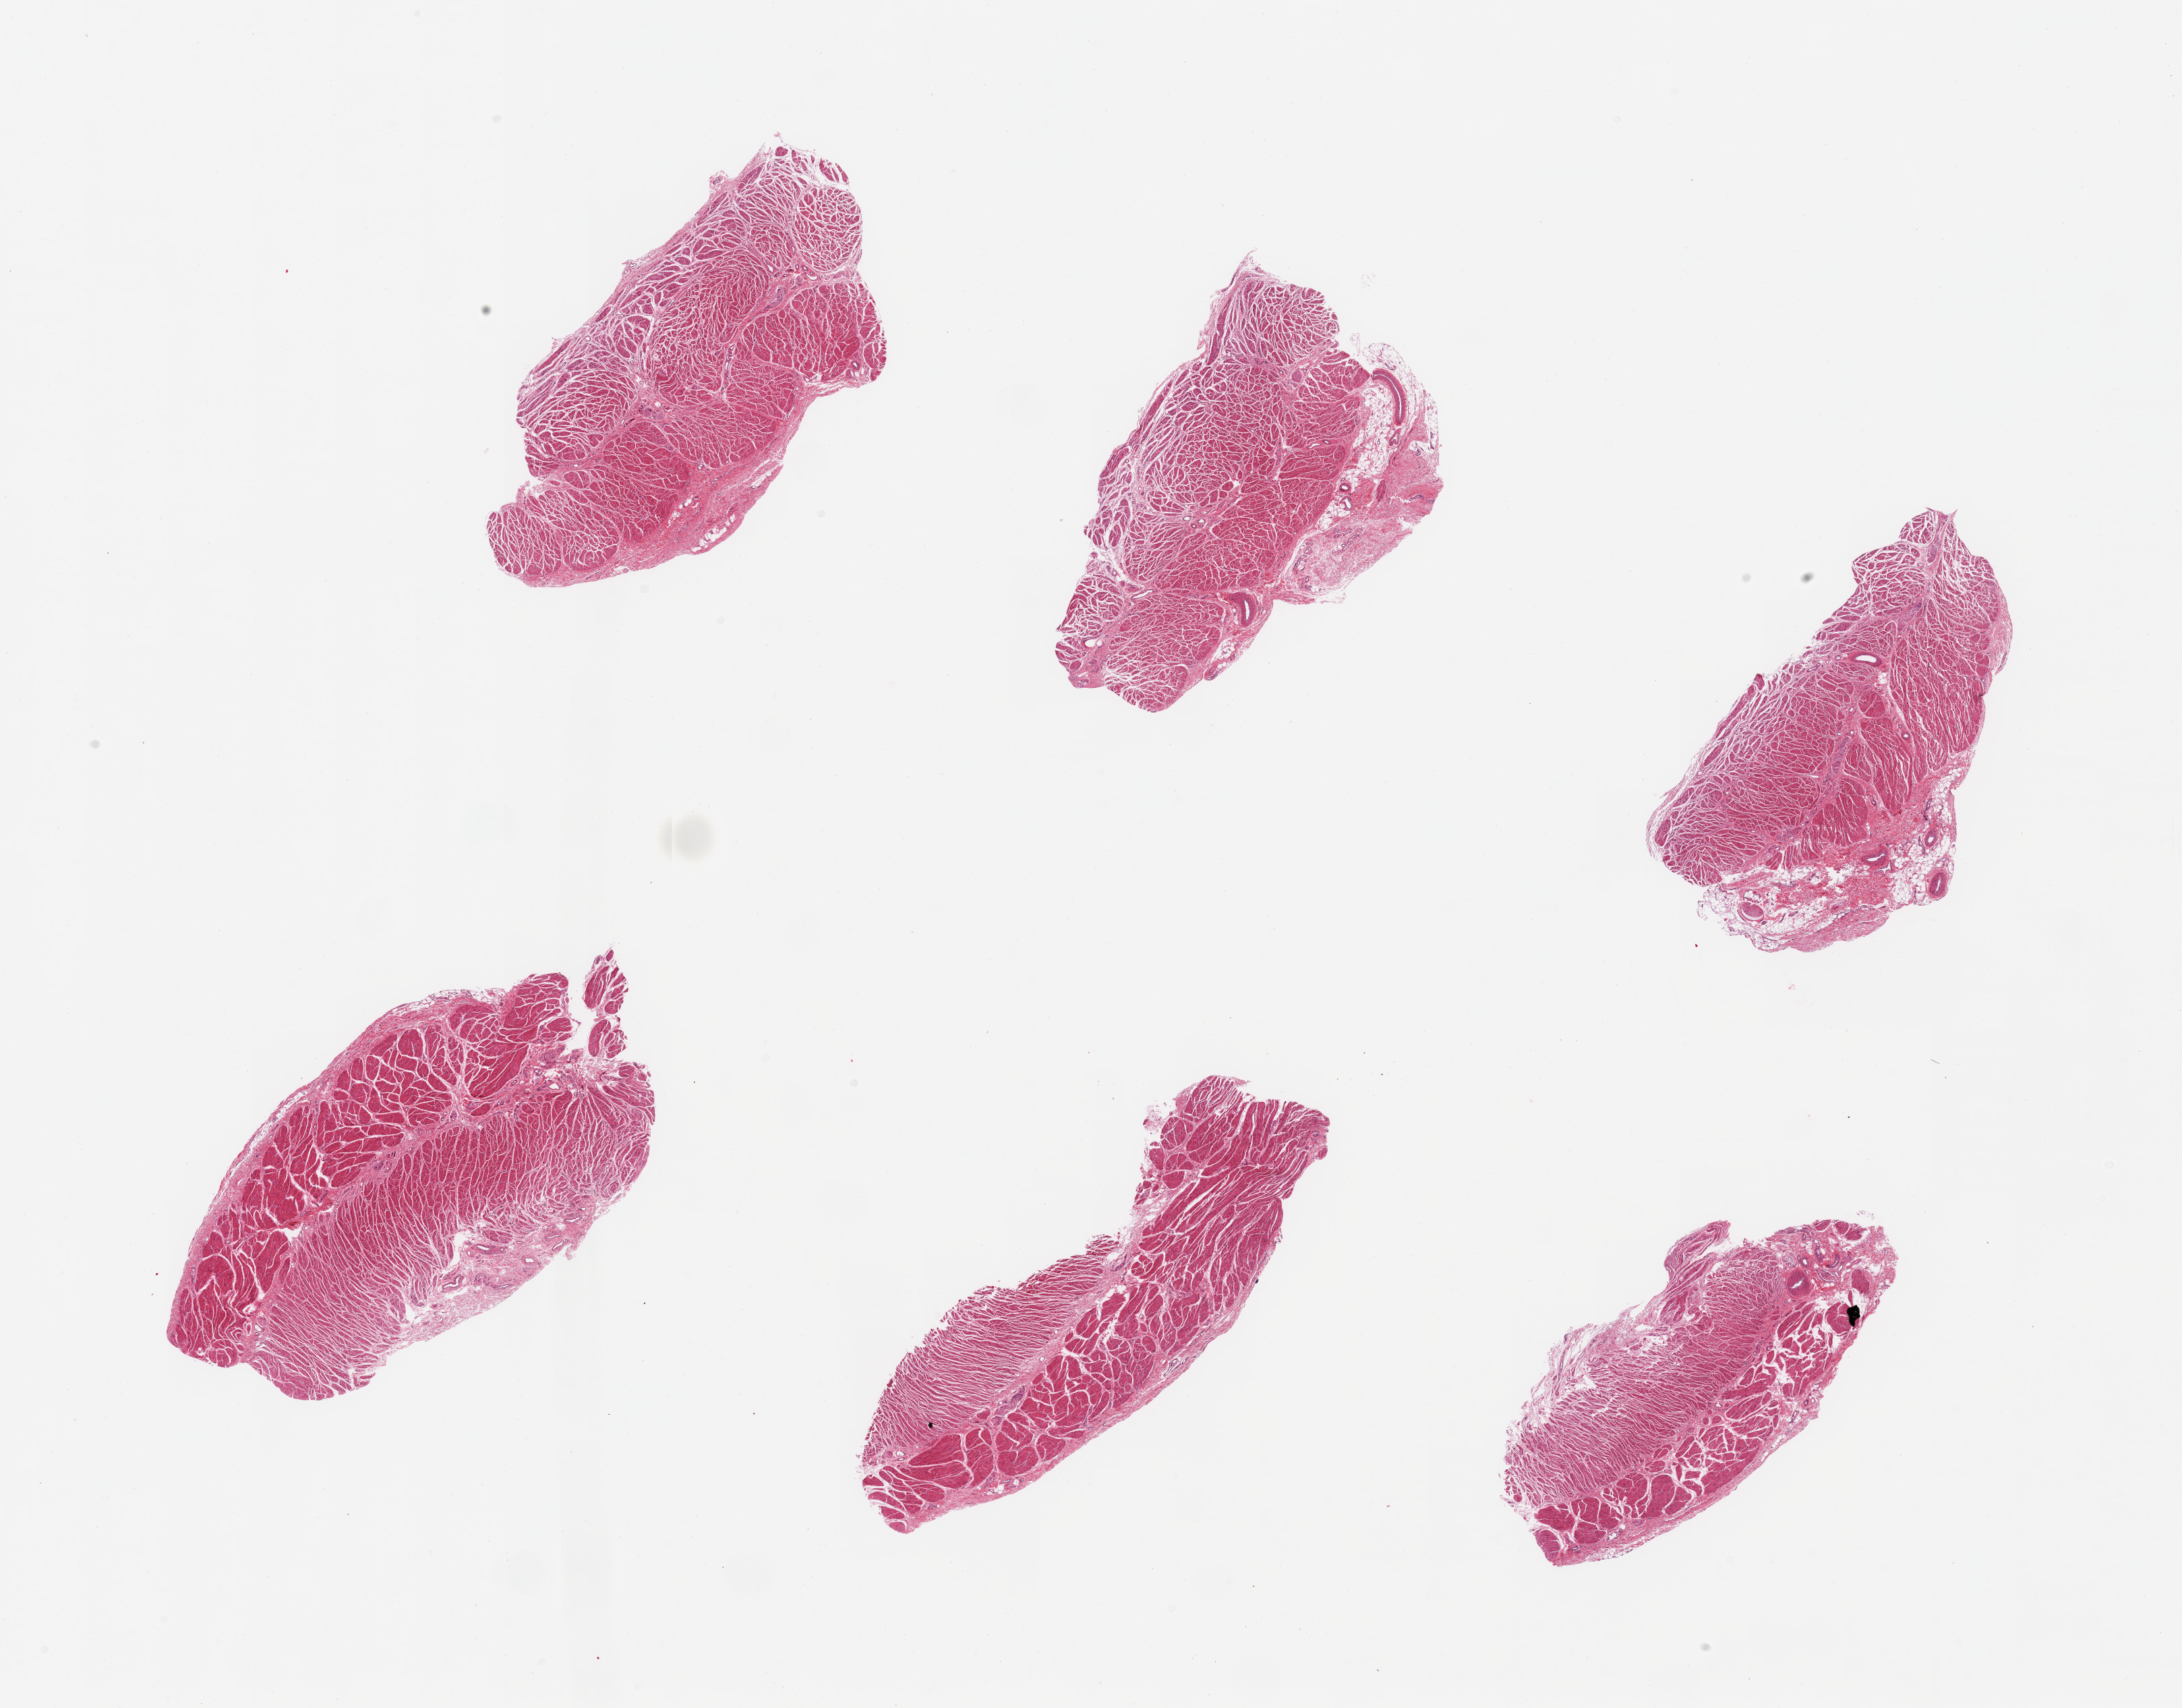
Whole-slide image, H&E stain, brightfield, shown as a low-resolution overview of the whole scanned area (about 25.6 x 20.0 mm). PAXgene-fixed paraffin-embedded (PFPE) section. Target tissue: gastroesophageal junction. Tissue donor sample. Donor sex: male.
Review note (as recorded): 6 pieces; target muscularis.